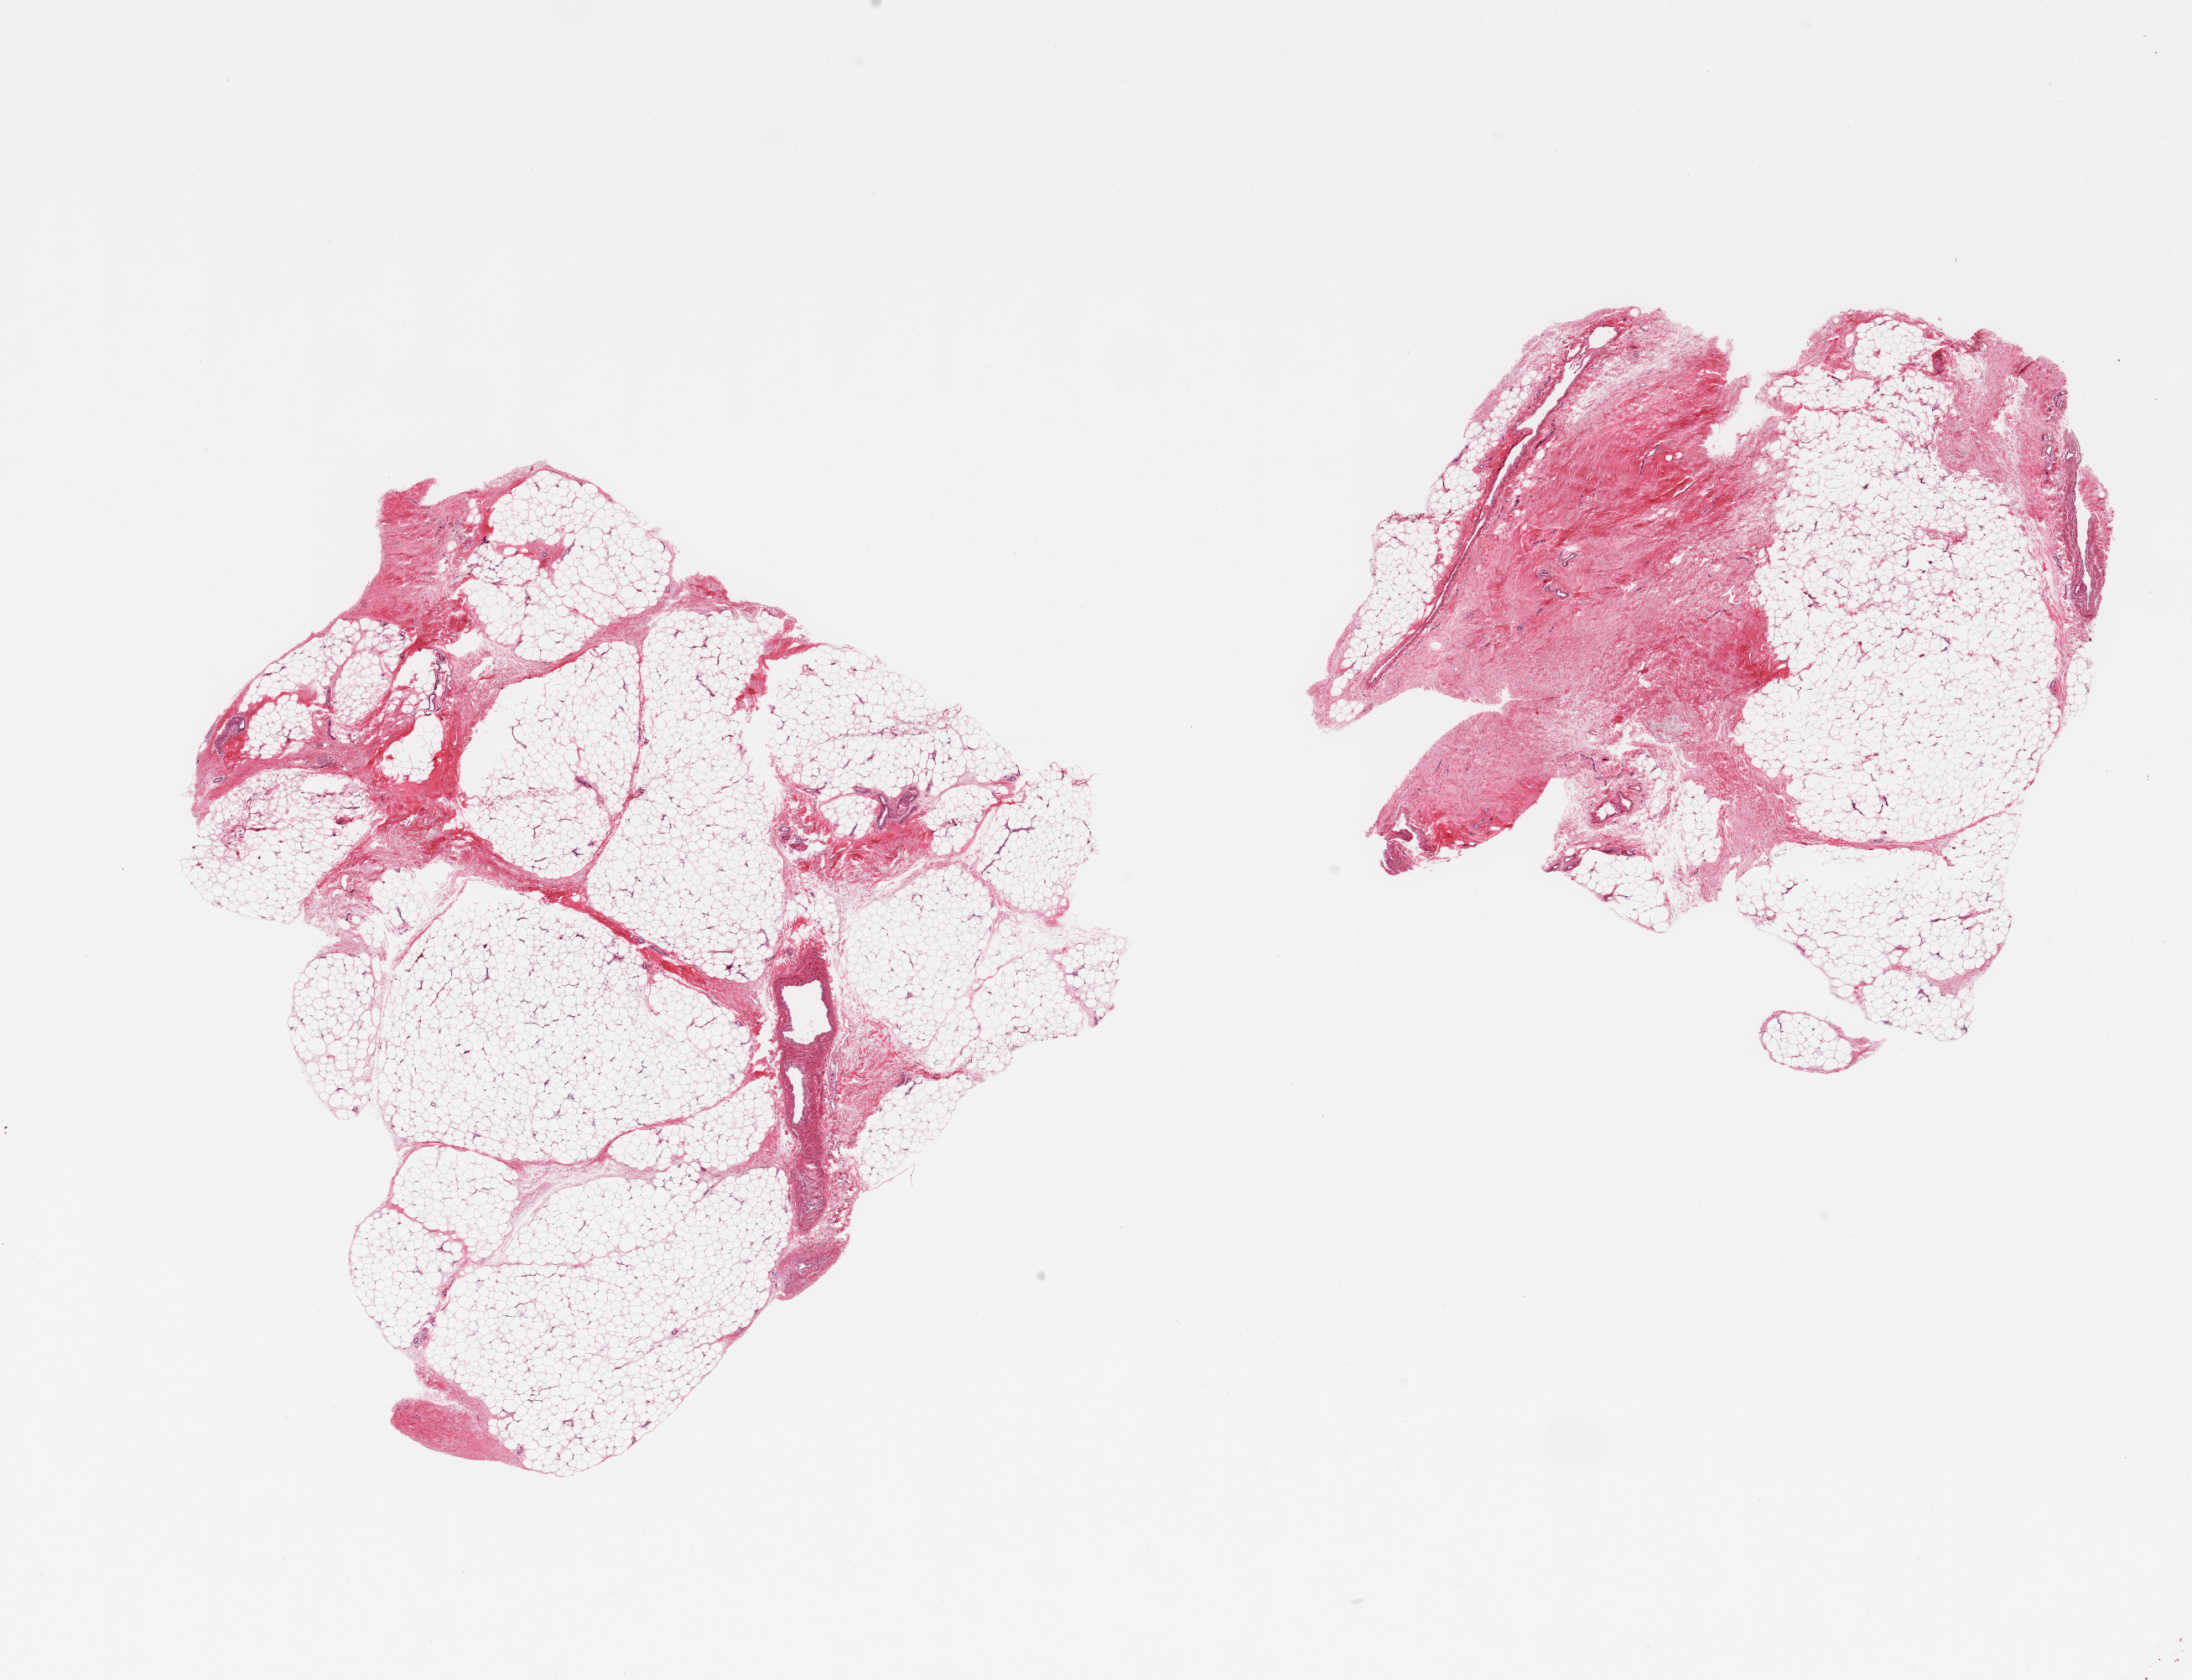
Whole-slide image, haematoxylin and eosin stain, brightfield — a low-resolution overview of the entire scanned area, about 20.7 x 15.8 mm (acquisition: 20x scan); PAXgene-fixed, paraffin-embedded tissue; target tissue: adipose tissue; donor tissue sample. Donor sex: male.
Reviewer comment on this tissue sample: 2 pieces; 10 & 40% fibrous content.